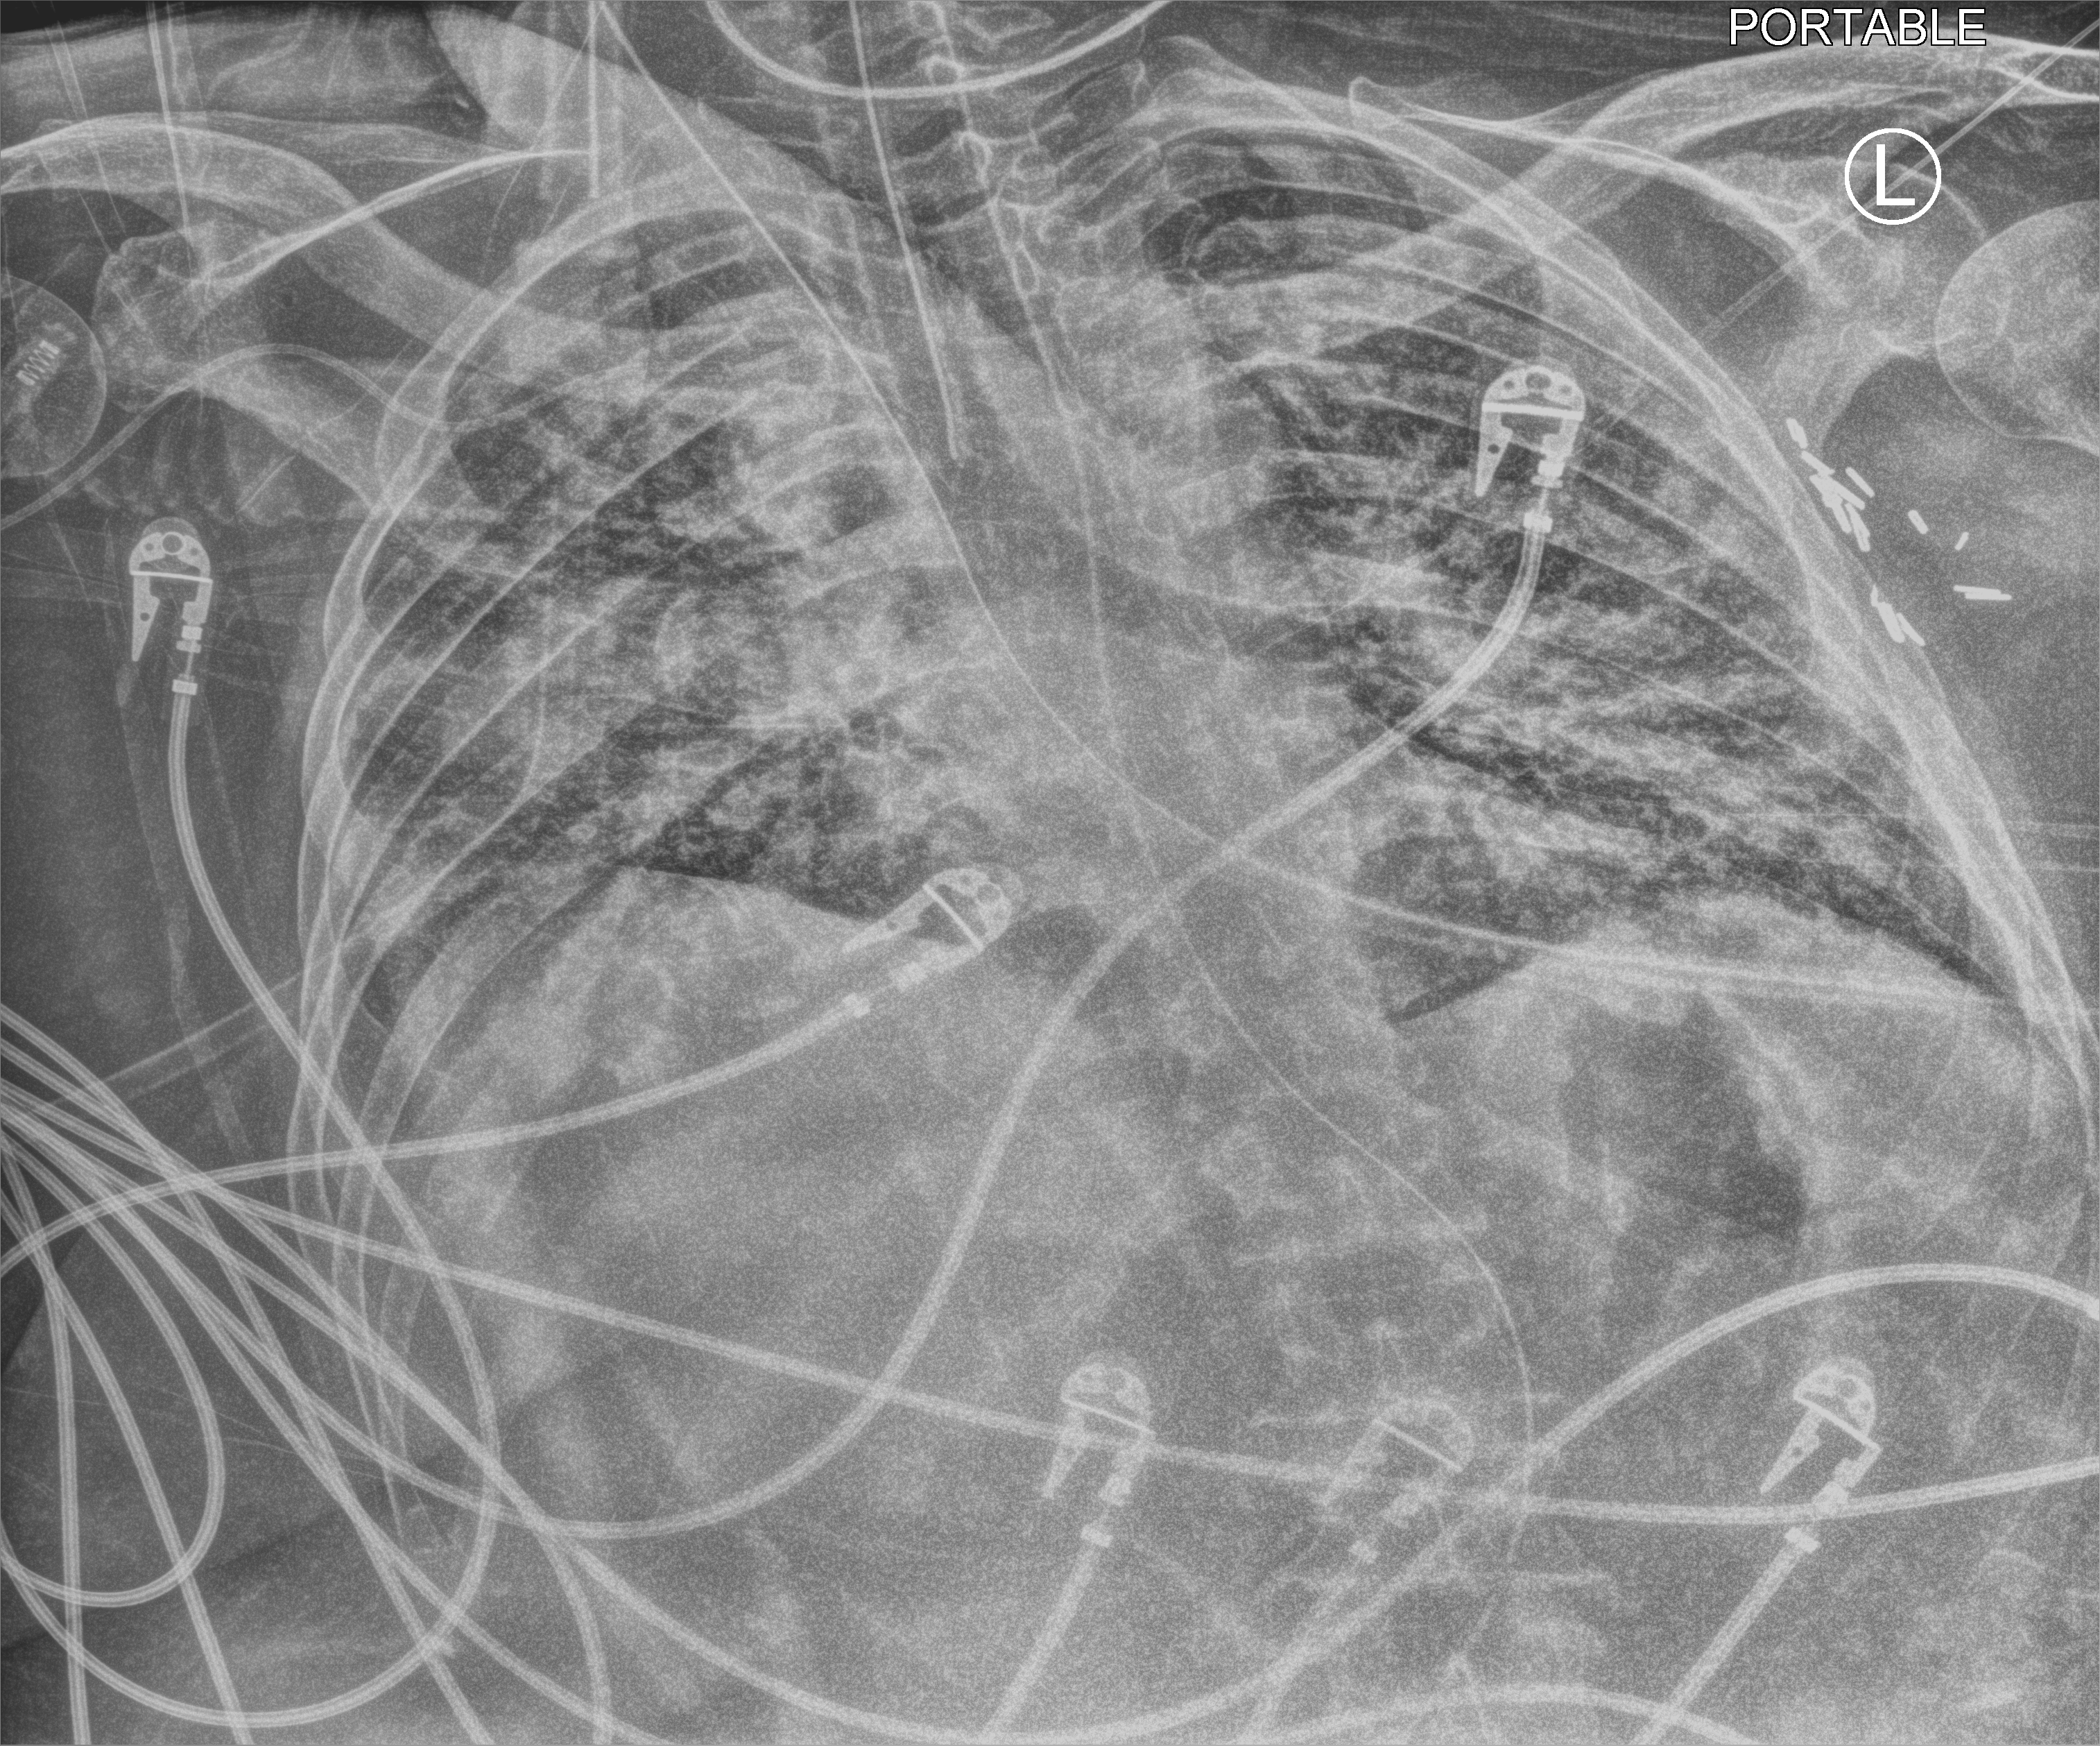
Bedside chest radiograph (computed radiography), anteroposterior (AP) projection. Female patient hospitalised with COVID-19, age 60–74 years.
Admission-level facts for this patient (not findings on this image; timing relative to this image not recorded):
- other chronic lung disease (admission record): no